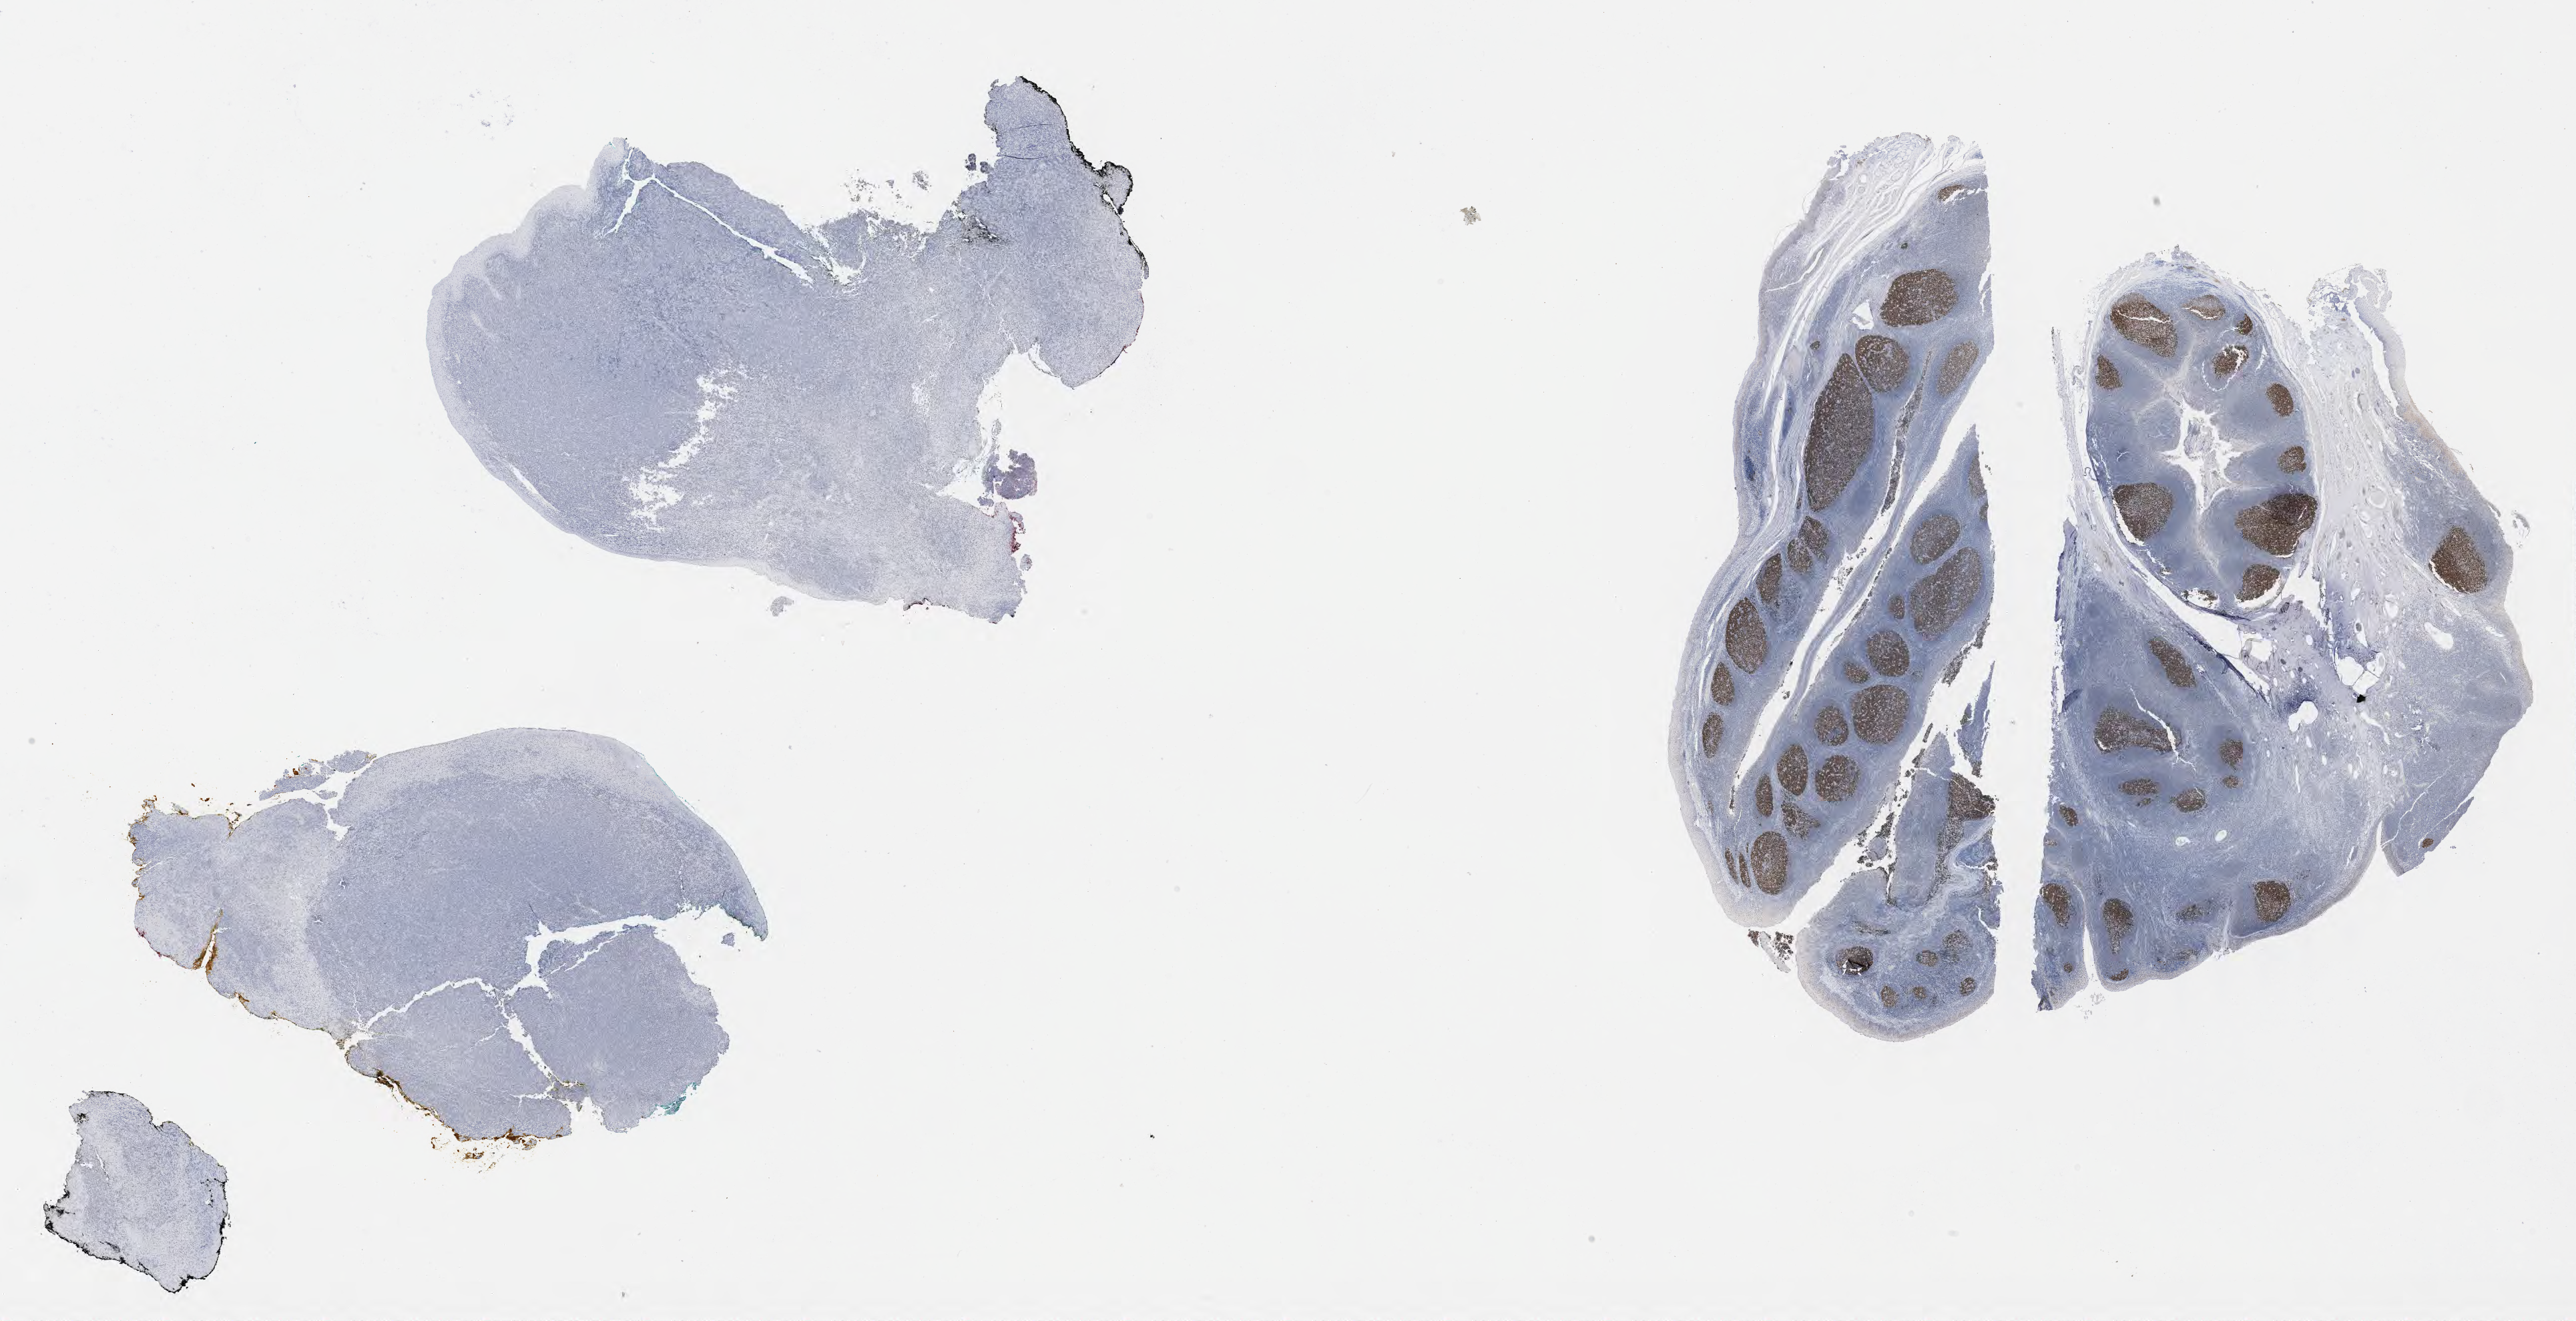
Immunohistochemistry (IHC) whole-slide image stained for BCL6, whole scanned area (about 31.2 x 16.0 mm) shown as a low-resolution overview; specimen: tumor tissue. Patient: male, aged 49.
Diagnosis: Diffuse large B-cell lymphoma, NOS.